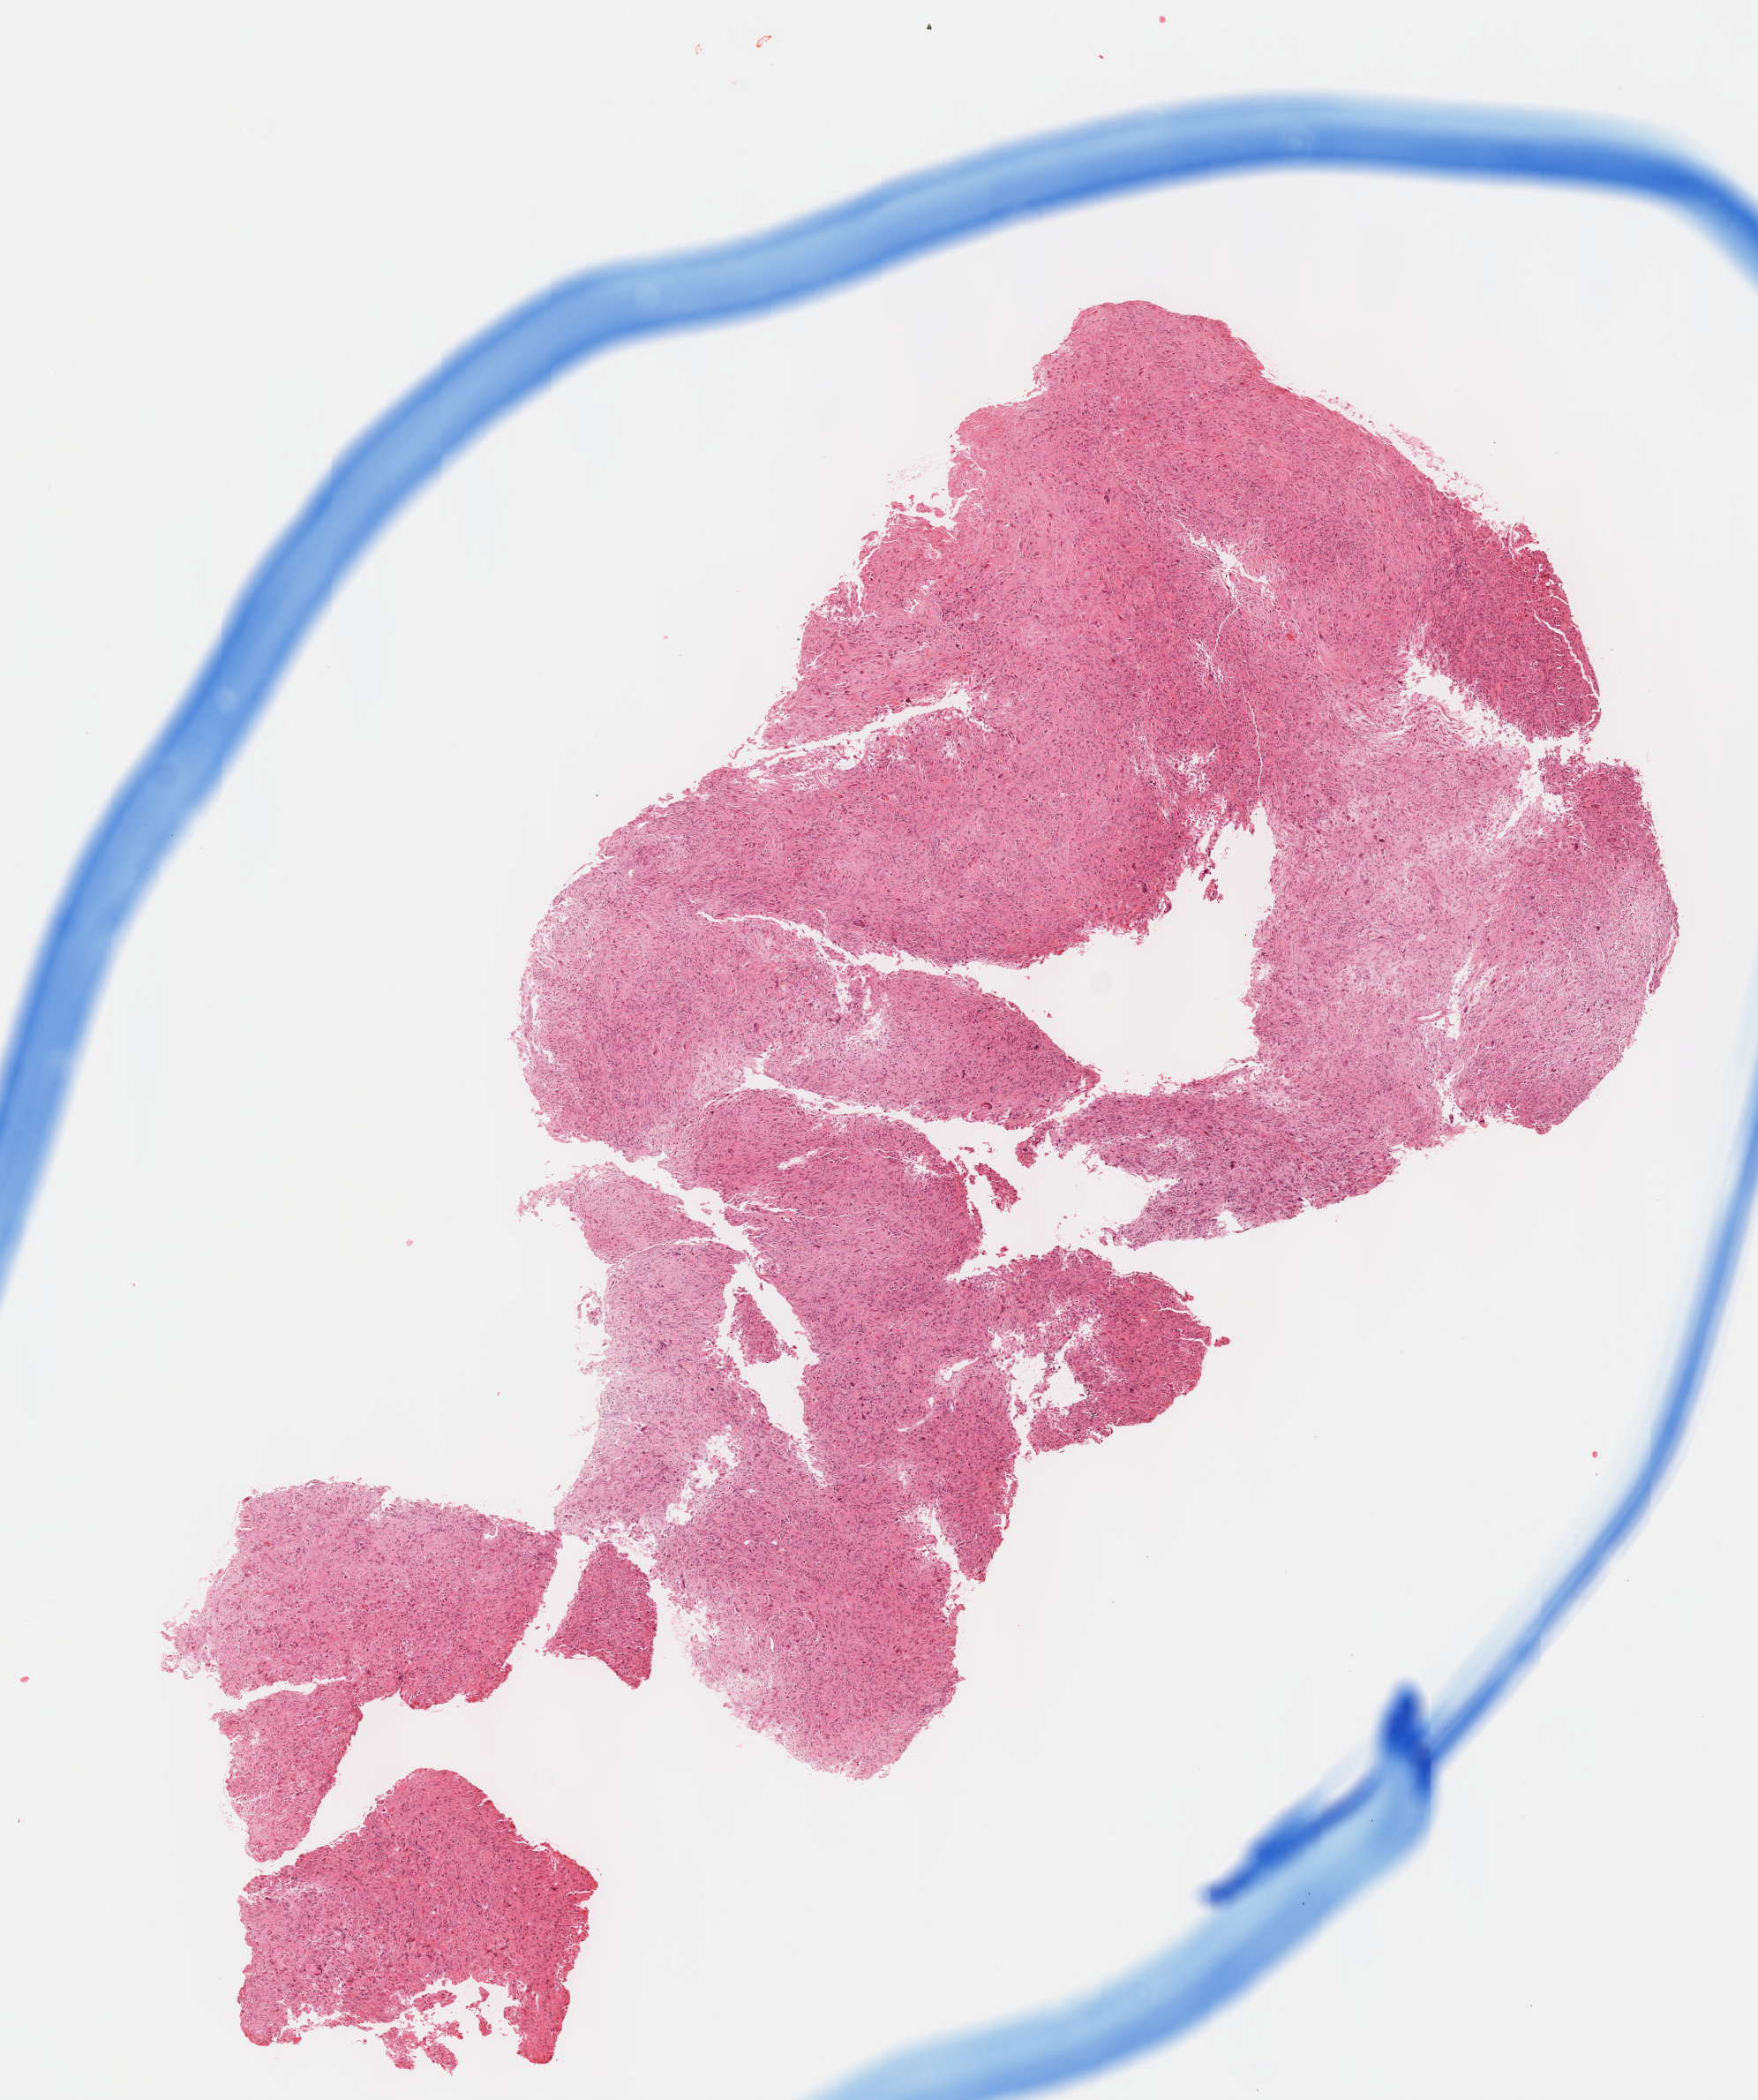
H&E-stained whole-slide image — shown as a low-resolution overview of the whole scanned area (about 8.0 x 9.6 mm, slide scanned at 40x), formalin-fixed paraffin-embedded (FFPE) diagnostic section, sample: primary tumour, brain. Male patient; age at initial diagnosis 48 years.
Histologic diagnosis: Glioblastoma.